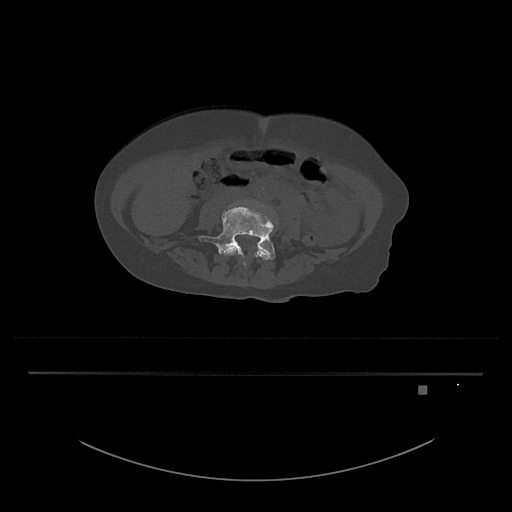
CT including the spine, one axial slice; reconstruction kernel Br40s/3; bone window (W 1800 / L 400 HU); 0.5 mm slice thickness; 512 × 512 image matrix. Patient: female, 57 years. From the clinical record (not read from this slice): primary cancer: cervical.
Structures marked on this image (semi-automatic segmentation, software-assisted and operator-edited):
- L4 vertebra: bounding box <223,246,271,269> (left, top, right, bottom; pixels)